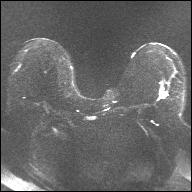
Breast MRI, one axial slice. Slice 16 of 32 in the series (ordered by position). Diffusion-weighted series; image 2 of 4 stored at this slice position (different b-values; order by instance number). 1.5 T. 4 mm slice thickness. 192 × 192 image matrix, field of view 360 × 360 mm. Female patient.
Annotated regions visible in this slice (outlined manually by an expert reader):
- tumour on diffusion-weighted imaging: box from (x=160, y=89) to (x=167, y=98) px